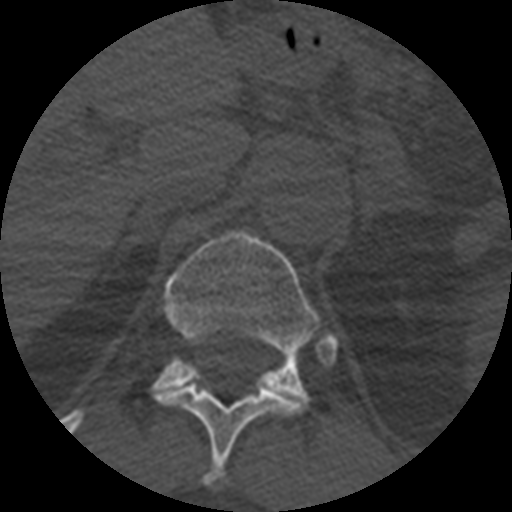
CT including the spine, one axial slice; reconstruction kernel STANDARD; bone window (W 1800 / L 400 HU); 512 × 512 image matrix, field of view 160 × 160 mm. Patient age 71 years. From the clinical record (not read from this slice): primary cancer: prostate.
Structures marked on this image (semi-automatic segmentation, software-assisted and operator-edited):
- T11 vertebra: box from (x=155, y=385) to (x=303, y=486) px
- T12 vertebra: (x=151, y=230)–(x=339, y=407)